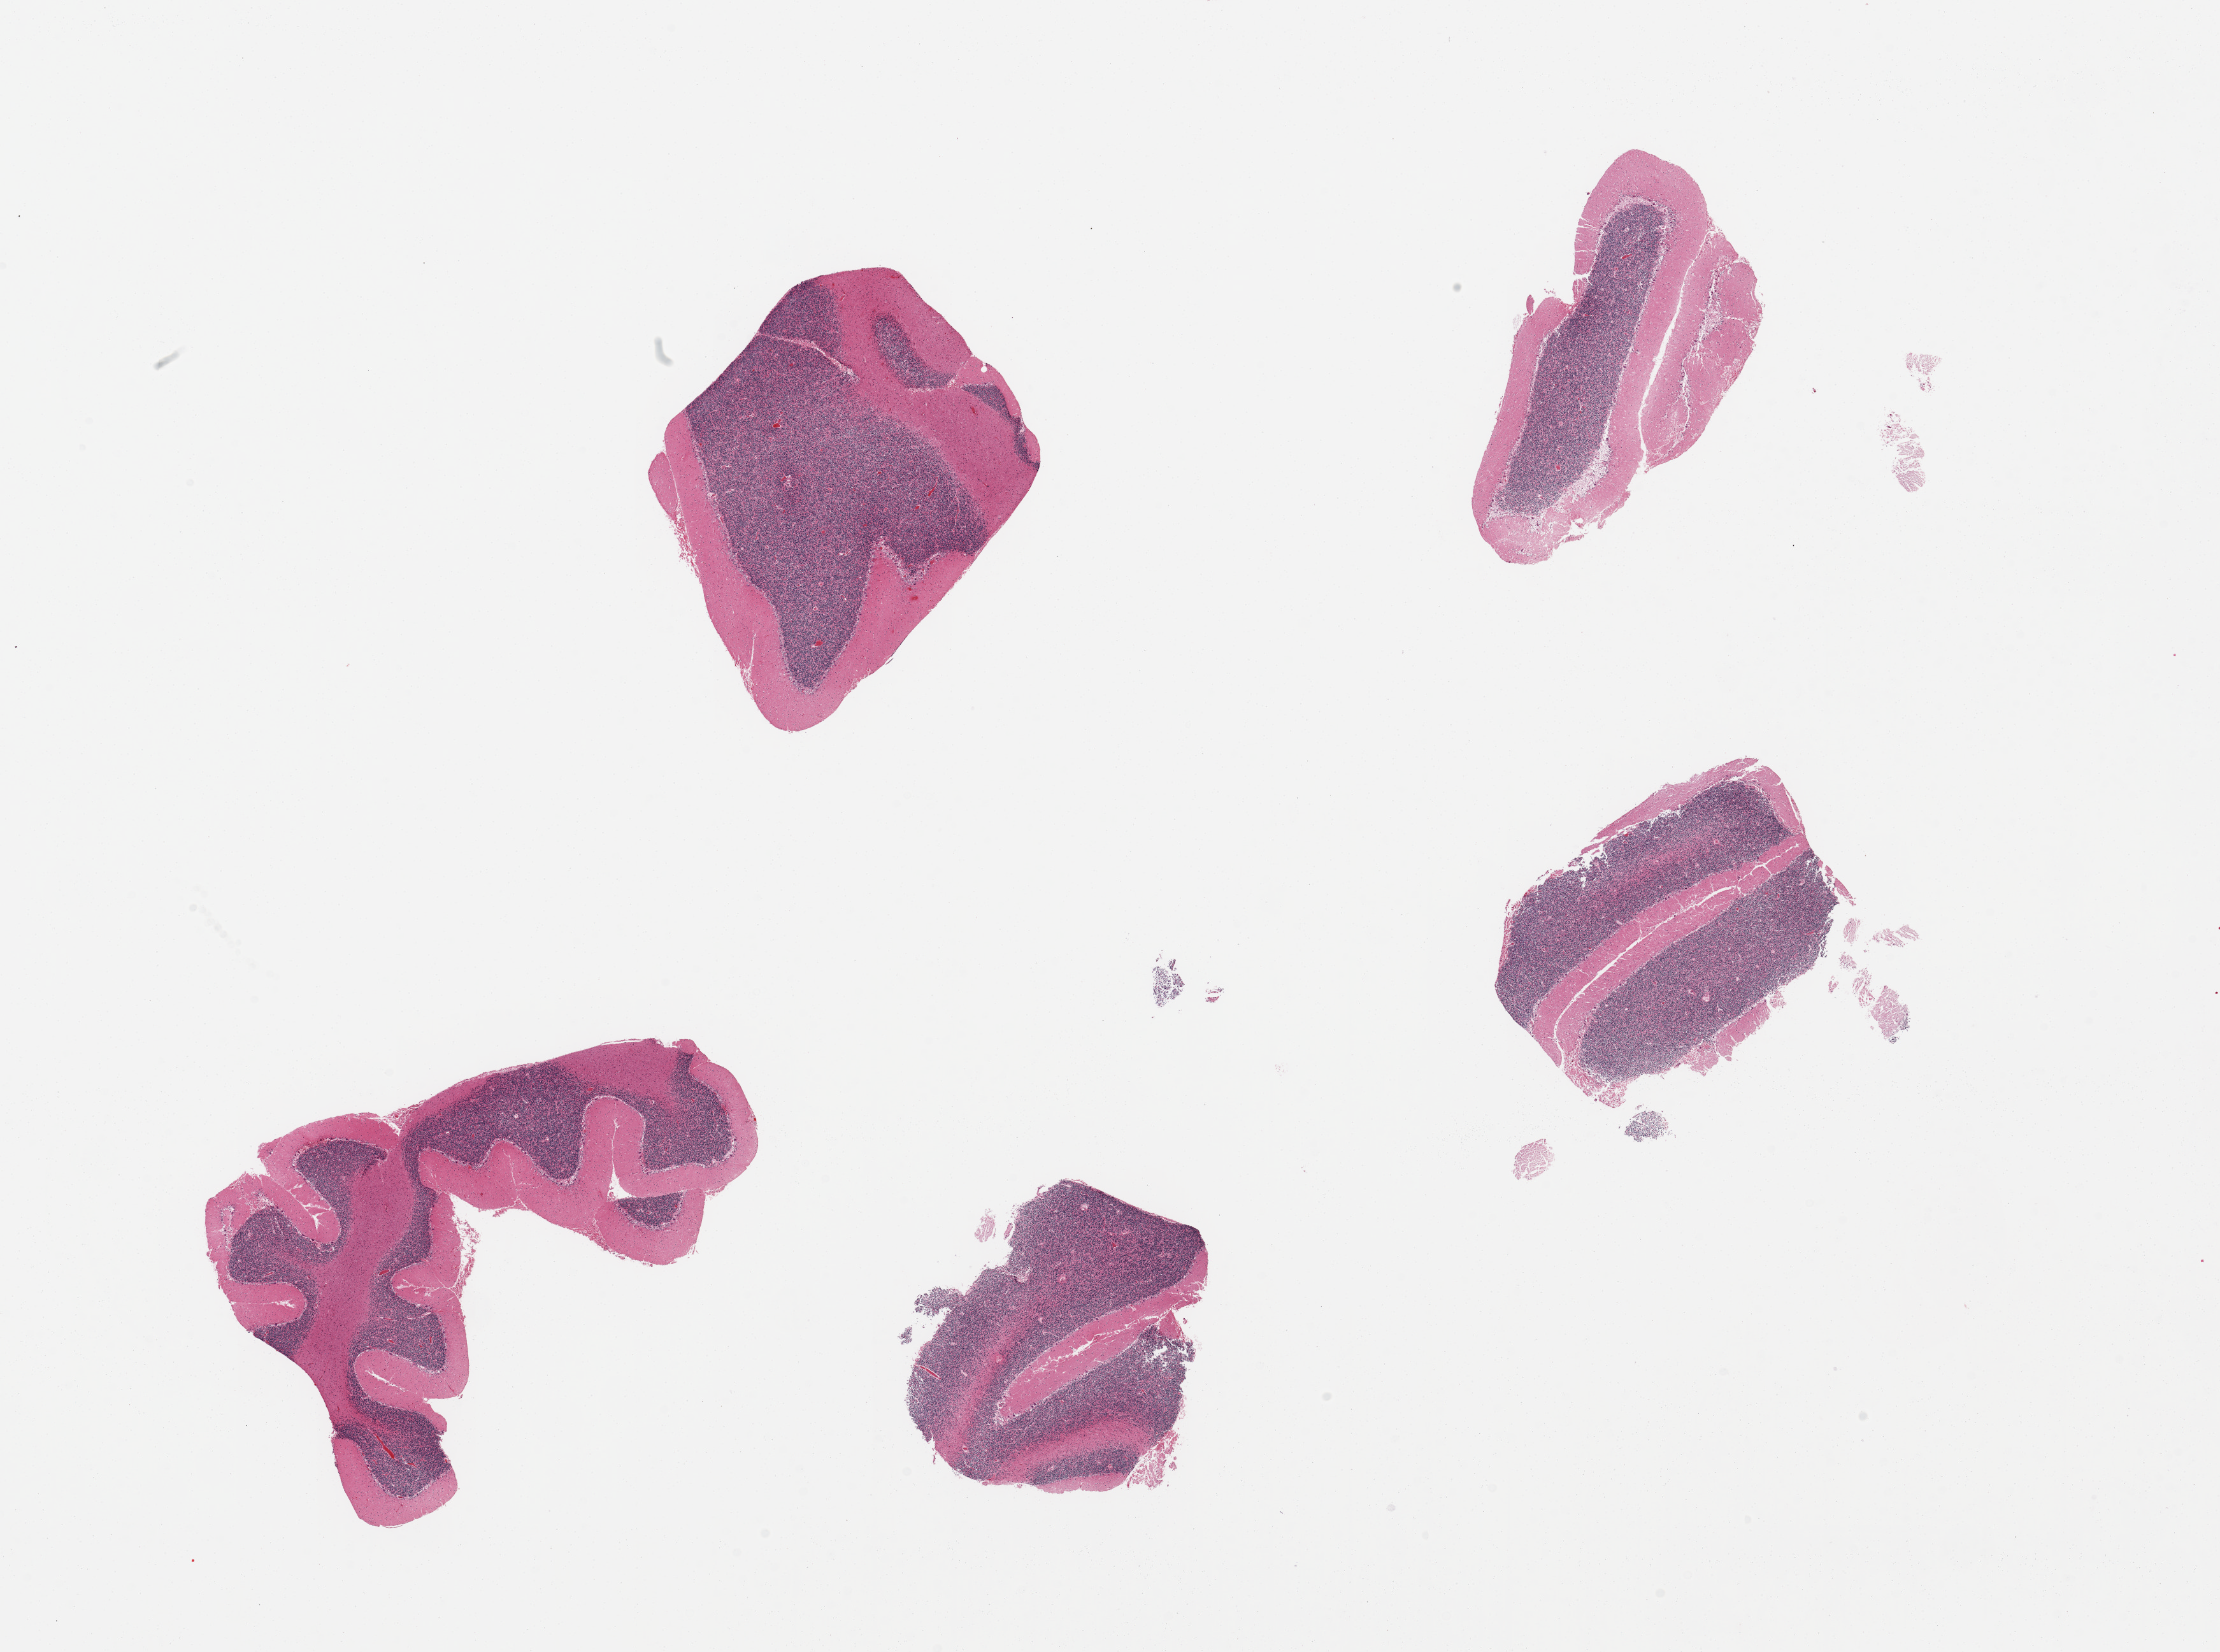
Digitized hematoxylin and eosin (H&E)-stained section, a low-resolution overview of the entire scanned area, about 27.6 x 20.5 mm, PAXgene-fixed paraffin-embedded (PFPE) section, target tissue: cerebellum, donor tissue sample.
• reviewer comment on this tissue sample: 5 pieces, no abnormalities